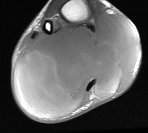
MRI of an extremity soft-tissue mass, one axial slice. Position 24 of 76 along the scan axis. MR volume resampled by the dataset authors to the PET/CT grid (not the native acquisition matrix). 3.27 mm slice thickness. 148 × 133 image matrix, field of view 145 × 130 mm. Male patient. From the clinical record (not read from this slice): histological type: liposarcoma - round cell; grade: high; site of the primary tumour: right calf.
Outlined on this slice (expert contour drawn on MRI and transferred to this co-registered scan by the dataset authors):
- gross tumour volume (mass): box from (x=13, y=14) to (x=139, y=115) px